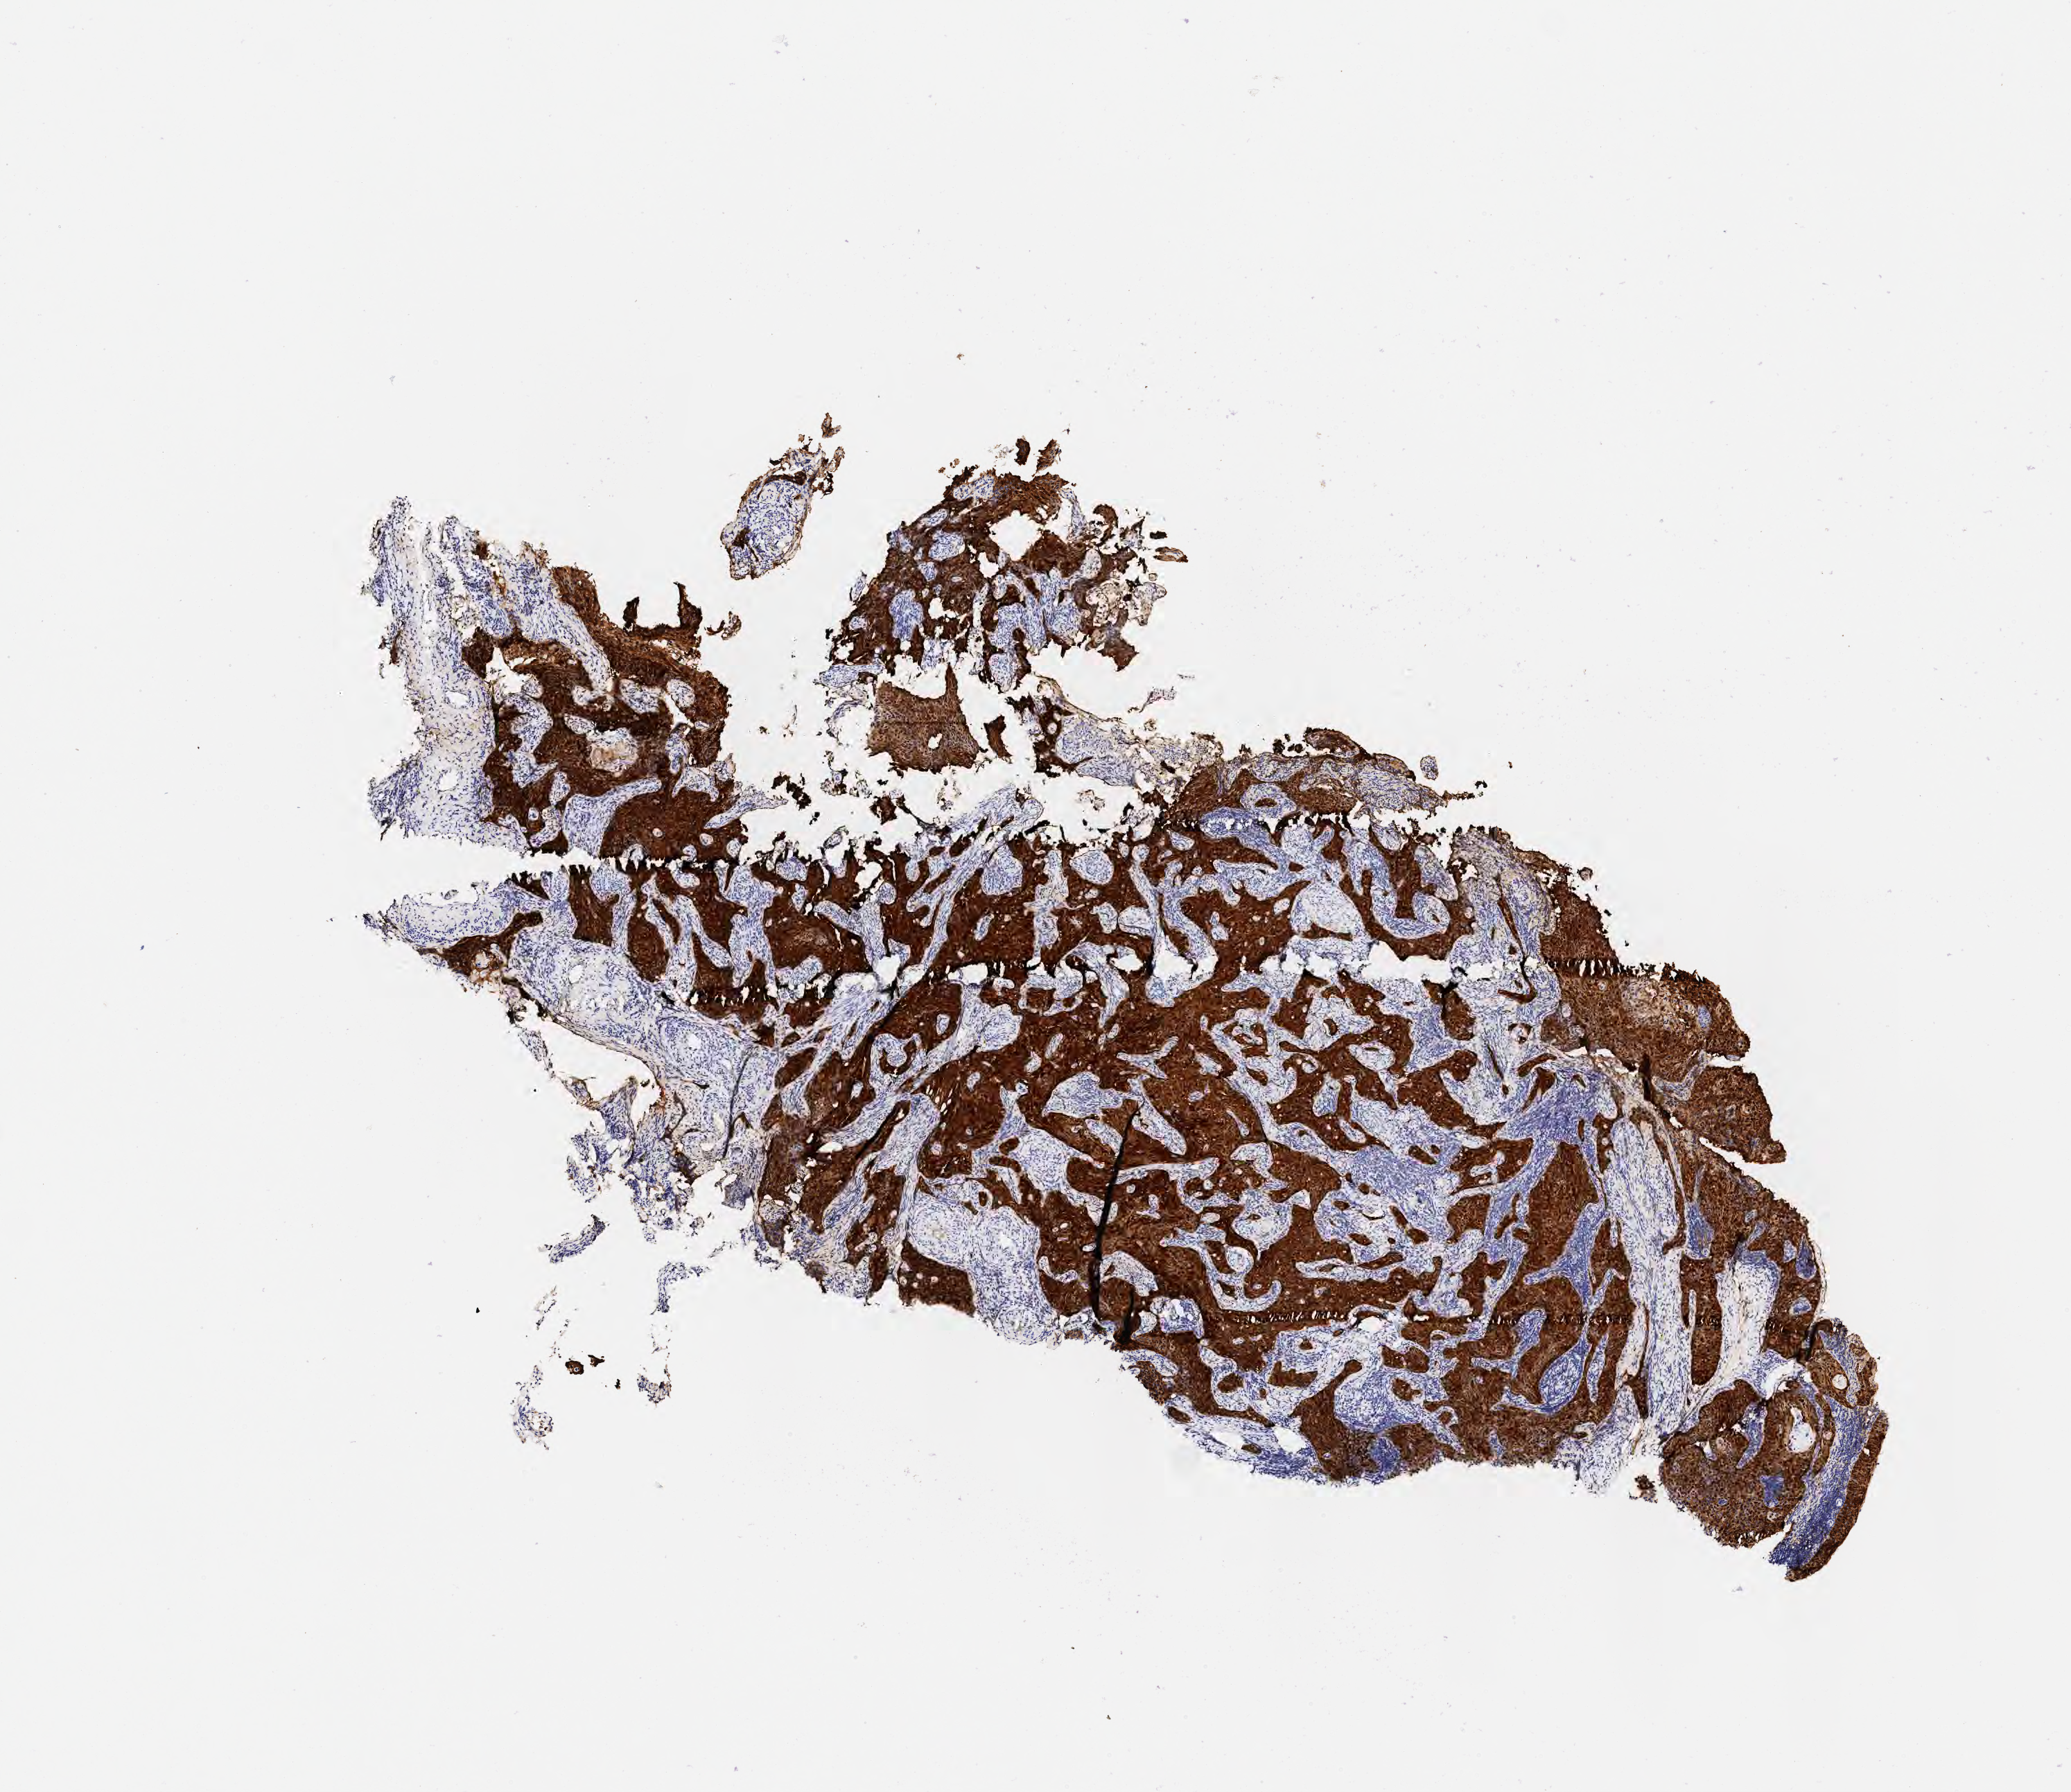
IHC for p16 (p16INK4a), whole-slide image — a low-resolution overview of the entire scanned area, about 6.0 x 5.2 mm, tumor tissue, anatomic site: cervix. Female patient, aged 58.
Diagnosis: Squamous cell carcinoma, large cell, nonkeratinizing, NOS.